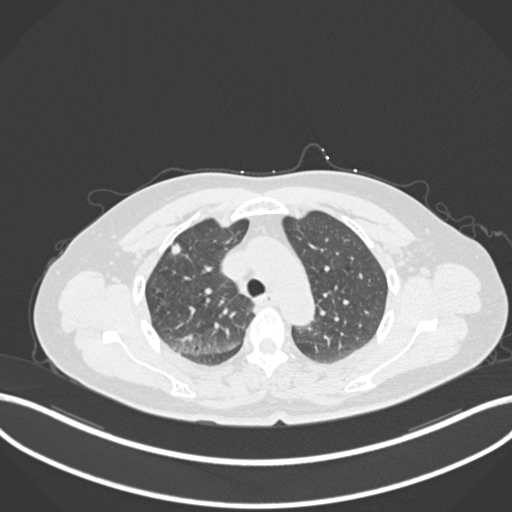
Chest CT, one axial slice; position 171 of 223 along the scan axis; 120 kVp; lung window (W 1500 / L -600 HU); 1 mm slice thickness; 512 × 512 image matrix, field of view 400 × 400 mm. Patient: female, 56 years. Case-level facts recorded for this patient, not image findings: clinical TNM (as recorded): T1c N0 M0.
Structures marked on this image (rectangle marked by the reading radiologist):
- lung tumour (recorded histology: adenocarcinoma): box from (x=167, y=240) to (x=189, y=258) px